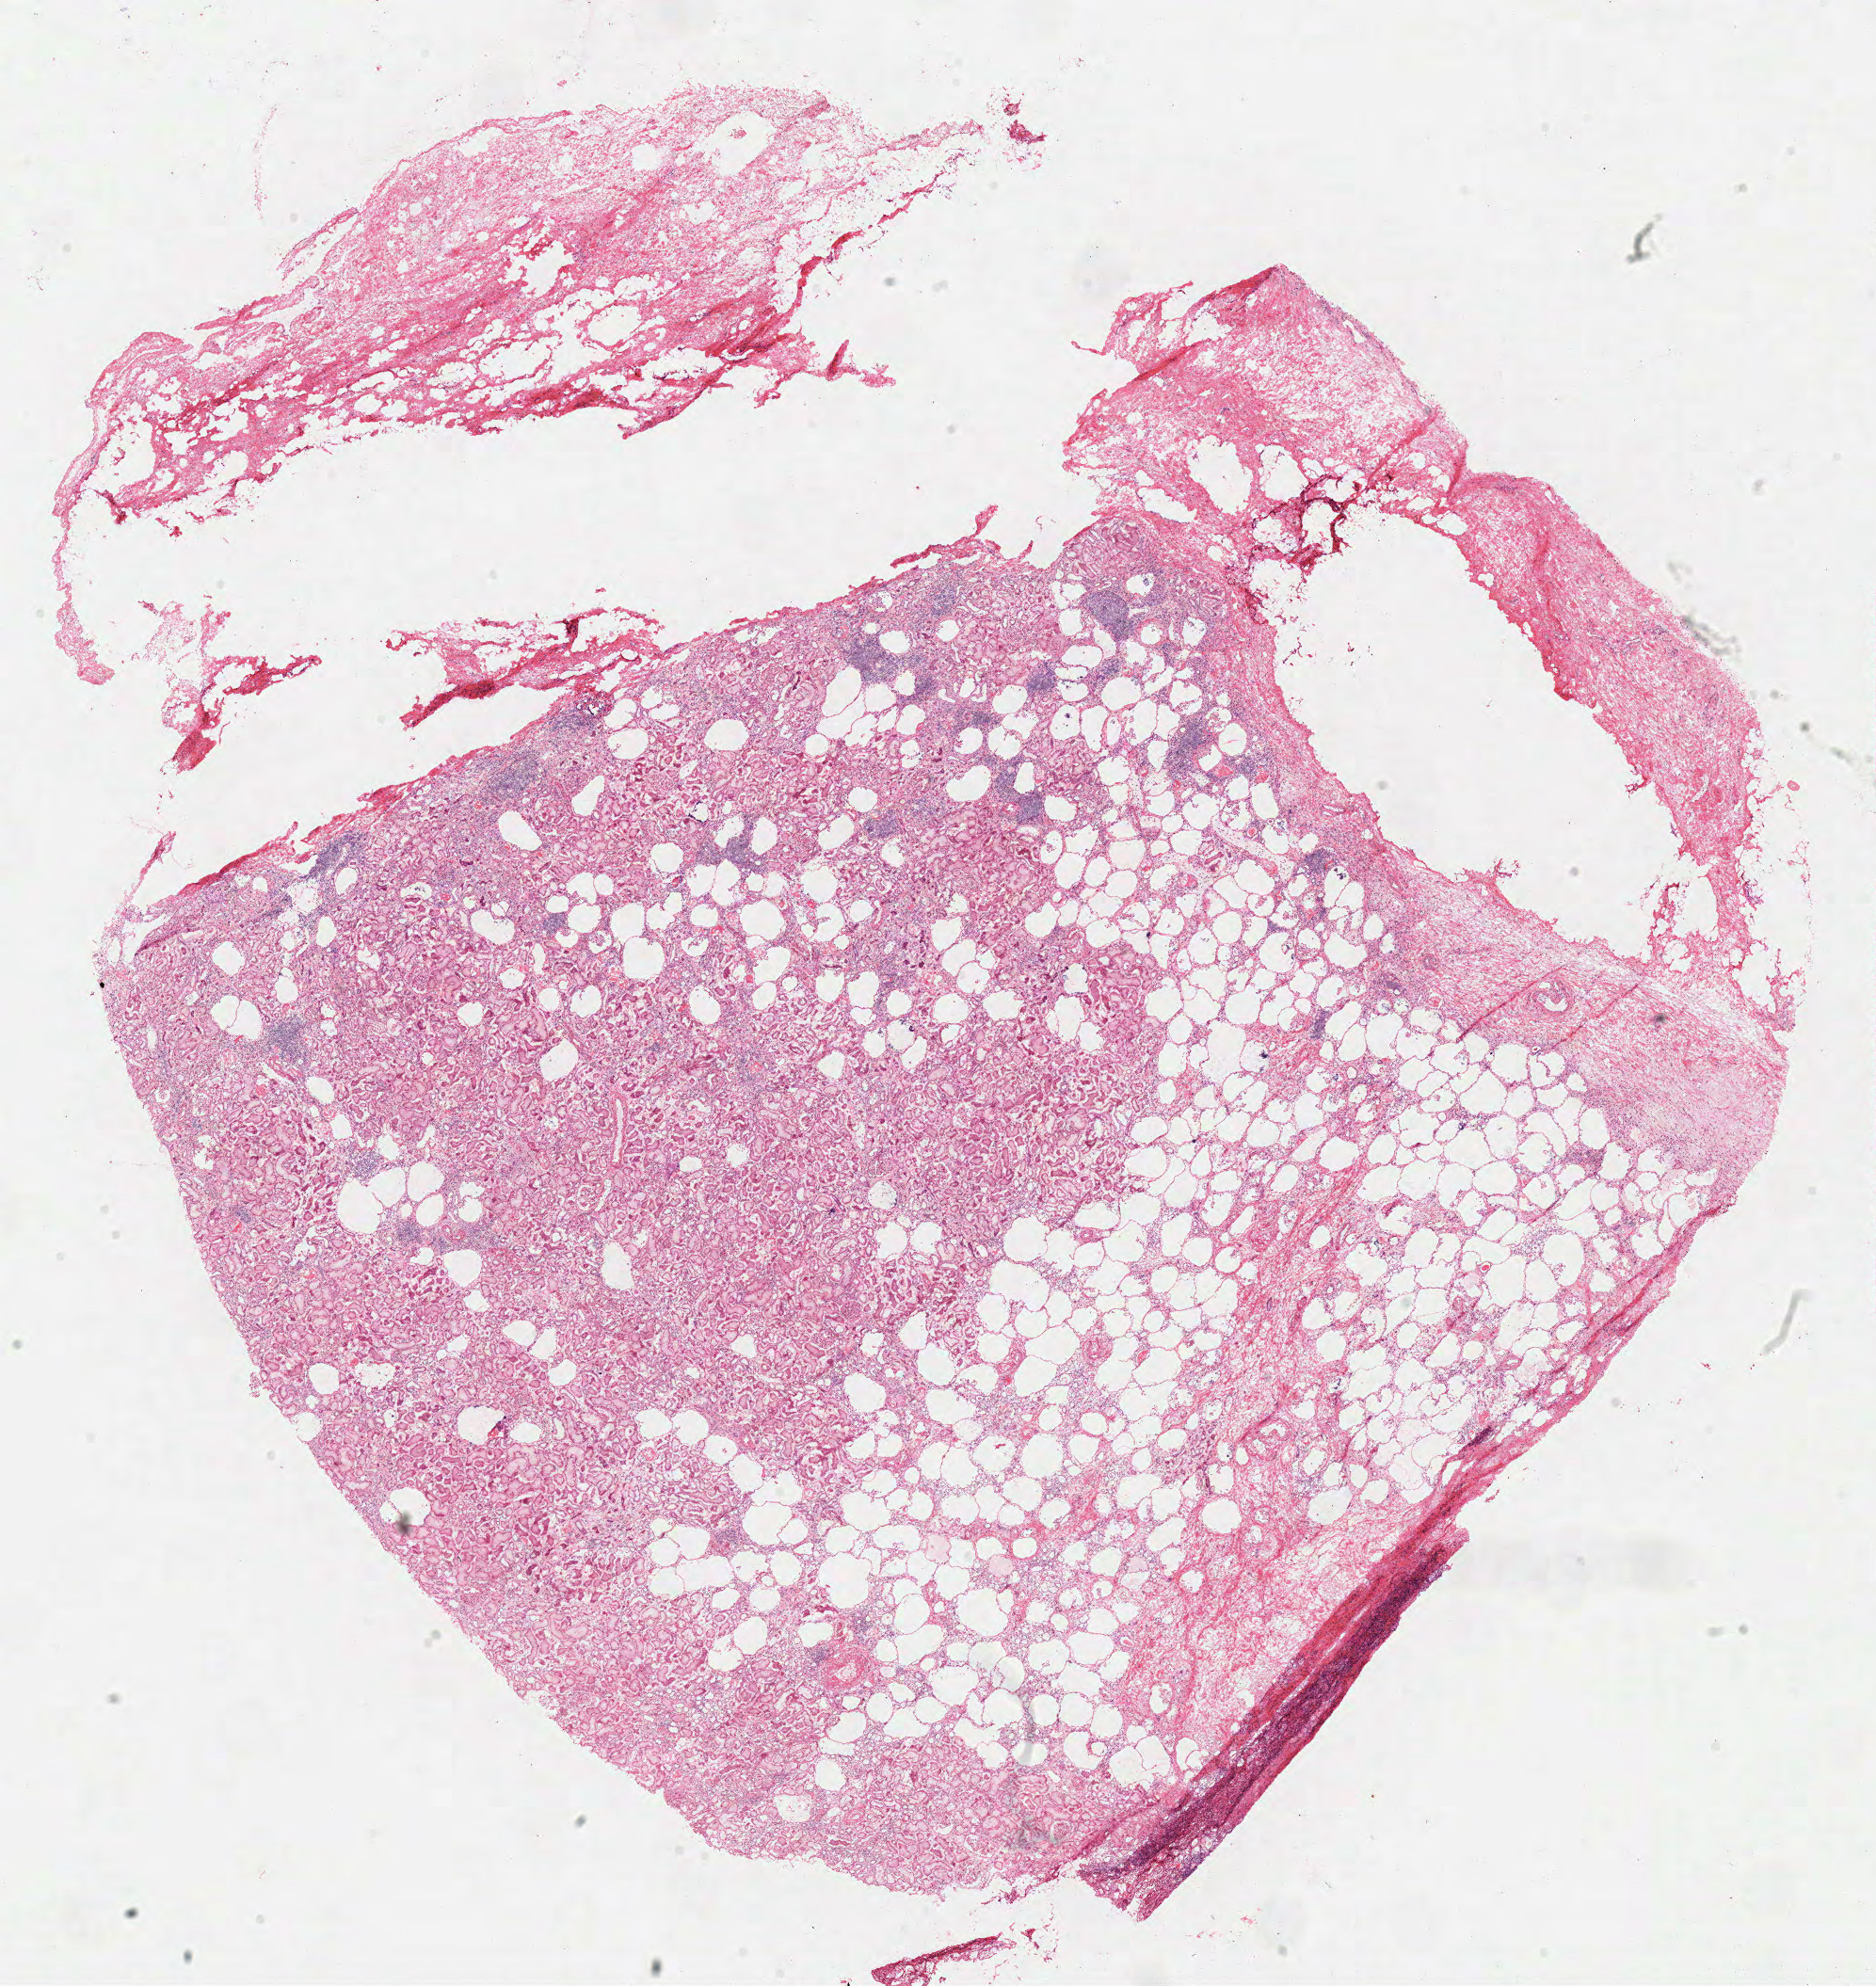
Whole-slide histology image, Hematoxylin and eosin (H&E) stained, a low-resolution overview of the entire scanned area, about 15.7 x 16.6 mm; frozen section from the top of the tissue portion; sample: solid tissue normal (non-tumour tissue), kidney. Male, age 69 years at initial diagnosis.
This section: solid tissue normal sample (biorepository sample class). Patient diagnosis: Papillary adenocarcinoma, NOS.